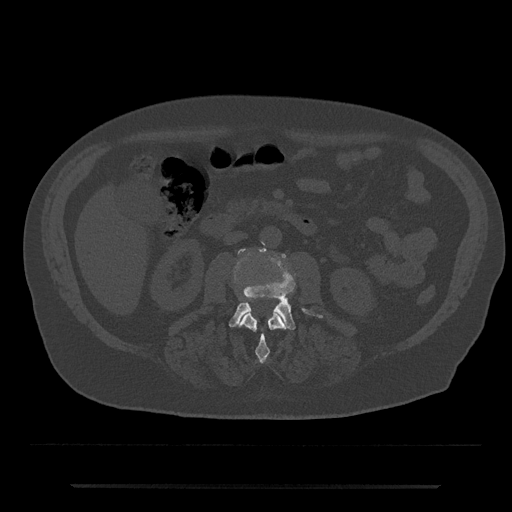
CT including the spine, one axial slice. Position 436 of 797 along the scan axis. Reconstruction kernel Br40s/3. 120 kVp. Bone window (W 1800 / L 400 HU). 512 × 512 image matrix, field of view 434 × 434 mm. Male patient, age 80 years. Case-level facts recorded for this patient, not image findings: primary cancer: prostate; vertebrae with lytic lesions (as recorded): L1, T11.
Annotated regions visible in this slice (semi-automatic segmentation, software-assisted and operator-edited):
- L2 vertebra: bounding box [x1, y1, x2, y2] px = [239, 310, 286, 363]
- L3 vertebra: [229, 248, 323, 330]